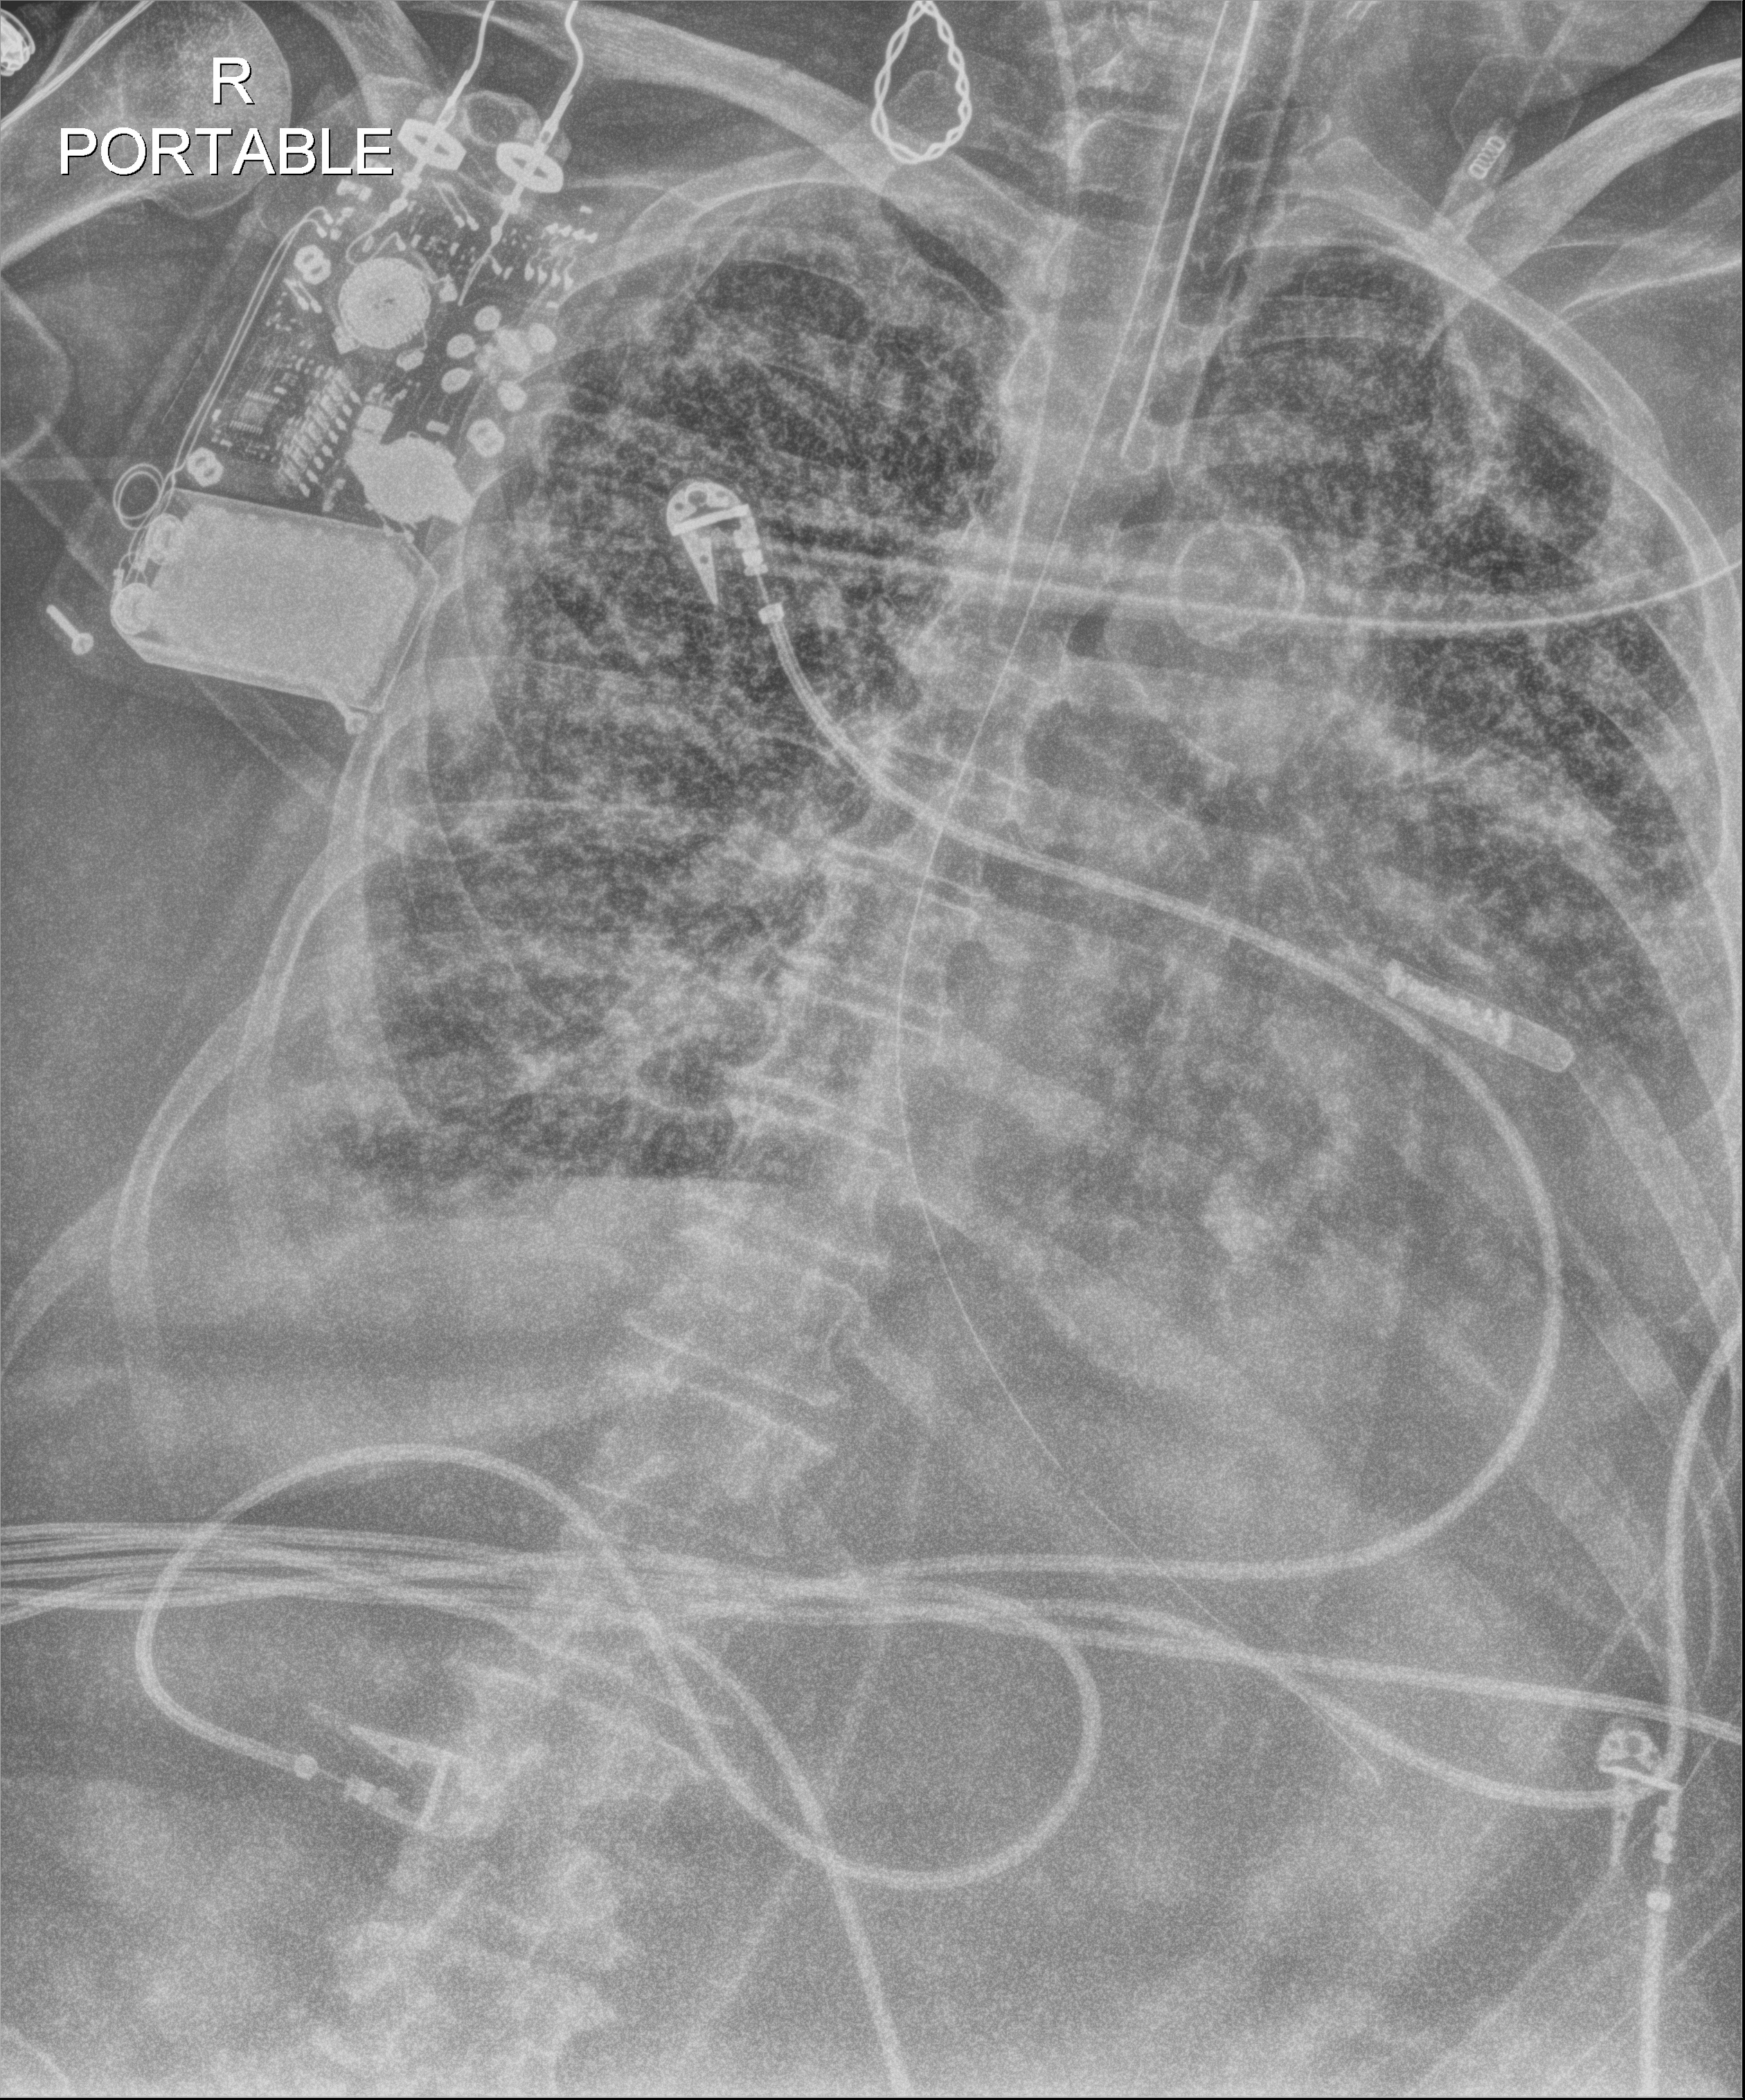
Chest X-ray (portable); anteroposterior (AP) projection. Patient hospitalised with COVID-19; female, aged 60–74 years.
Hospital-stay facts (about this admission, not read from this image; timing relative to this image not recorded):
- hypertension (admission record): yes
- mechanically ventilated during this hospital stay: yes